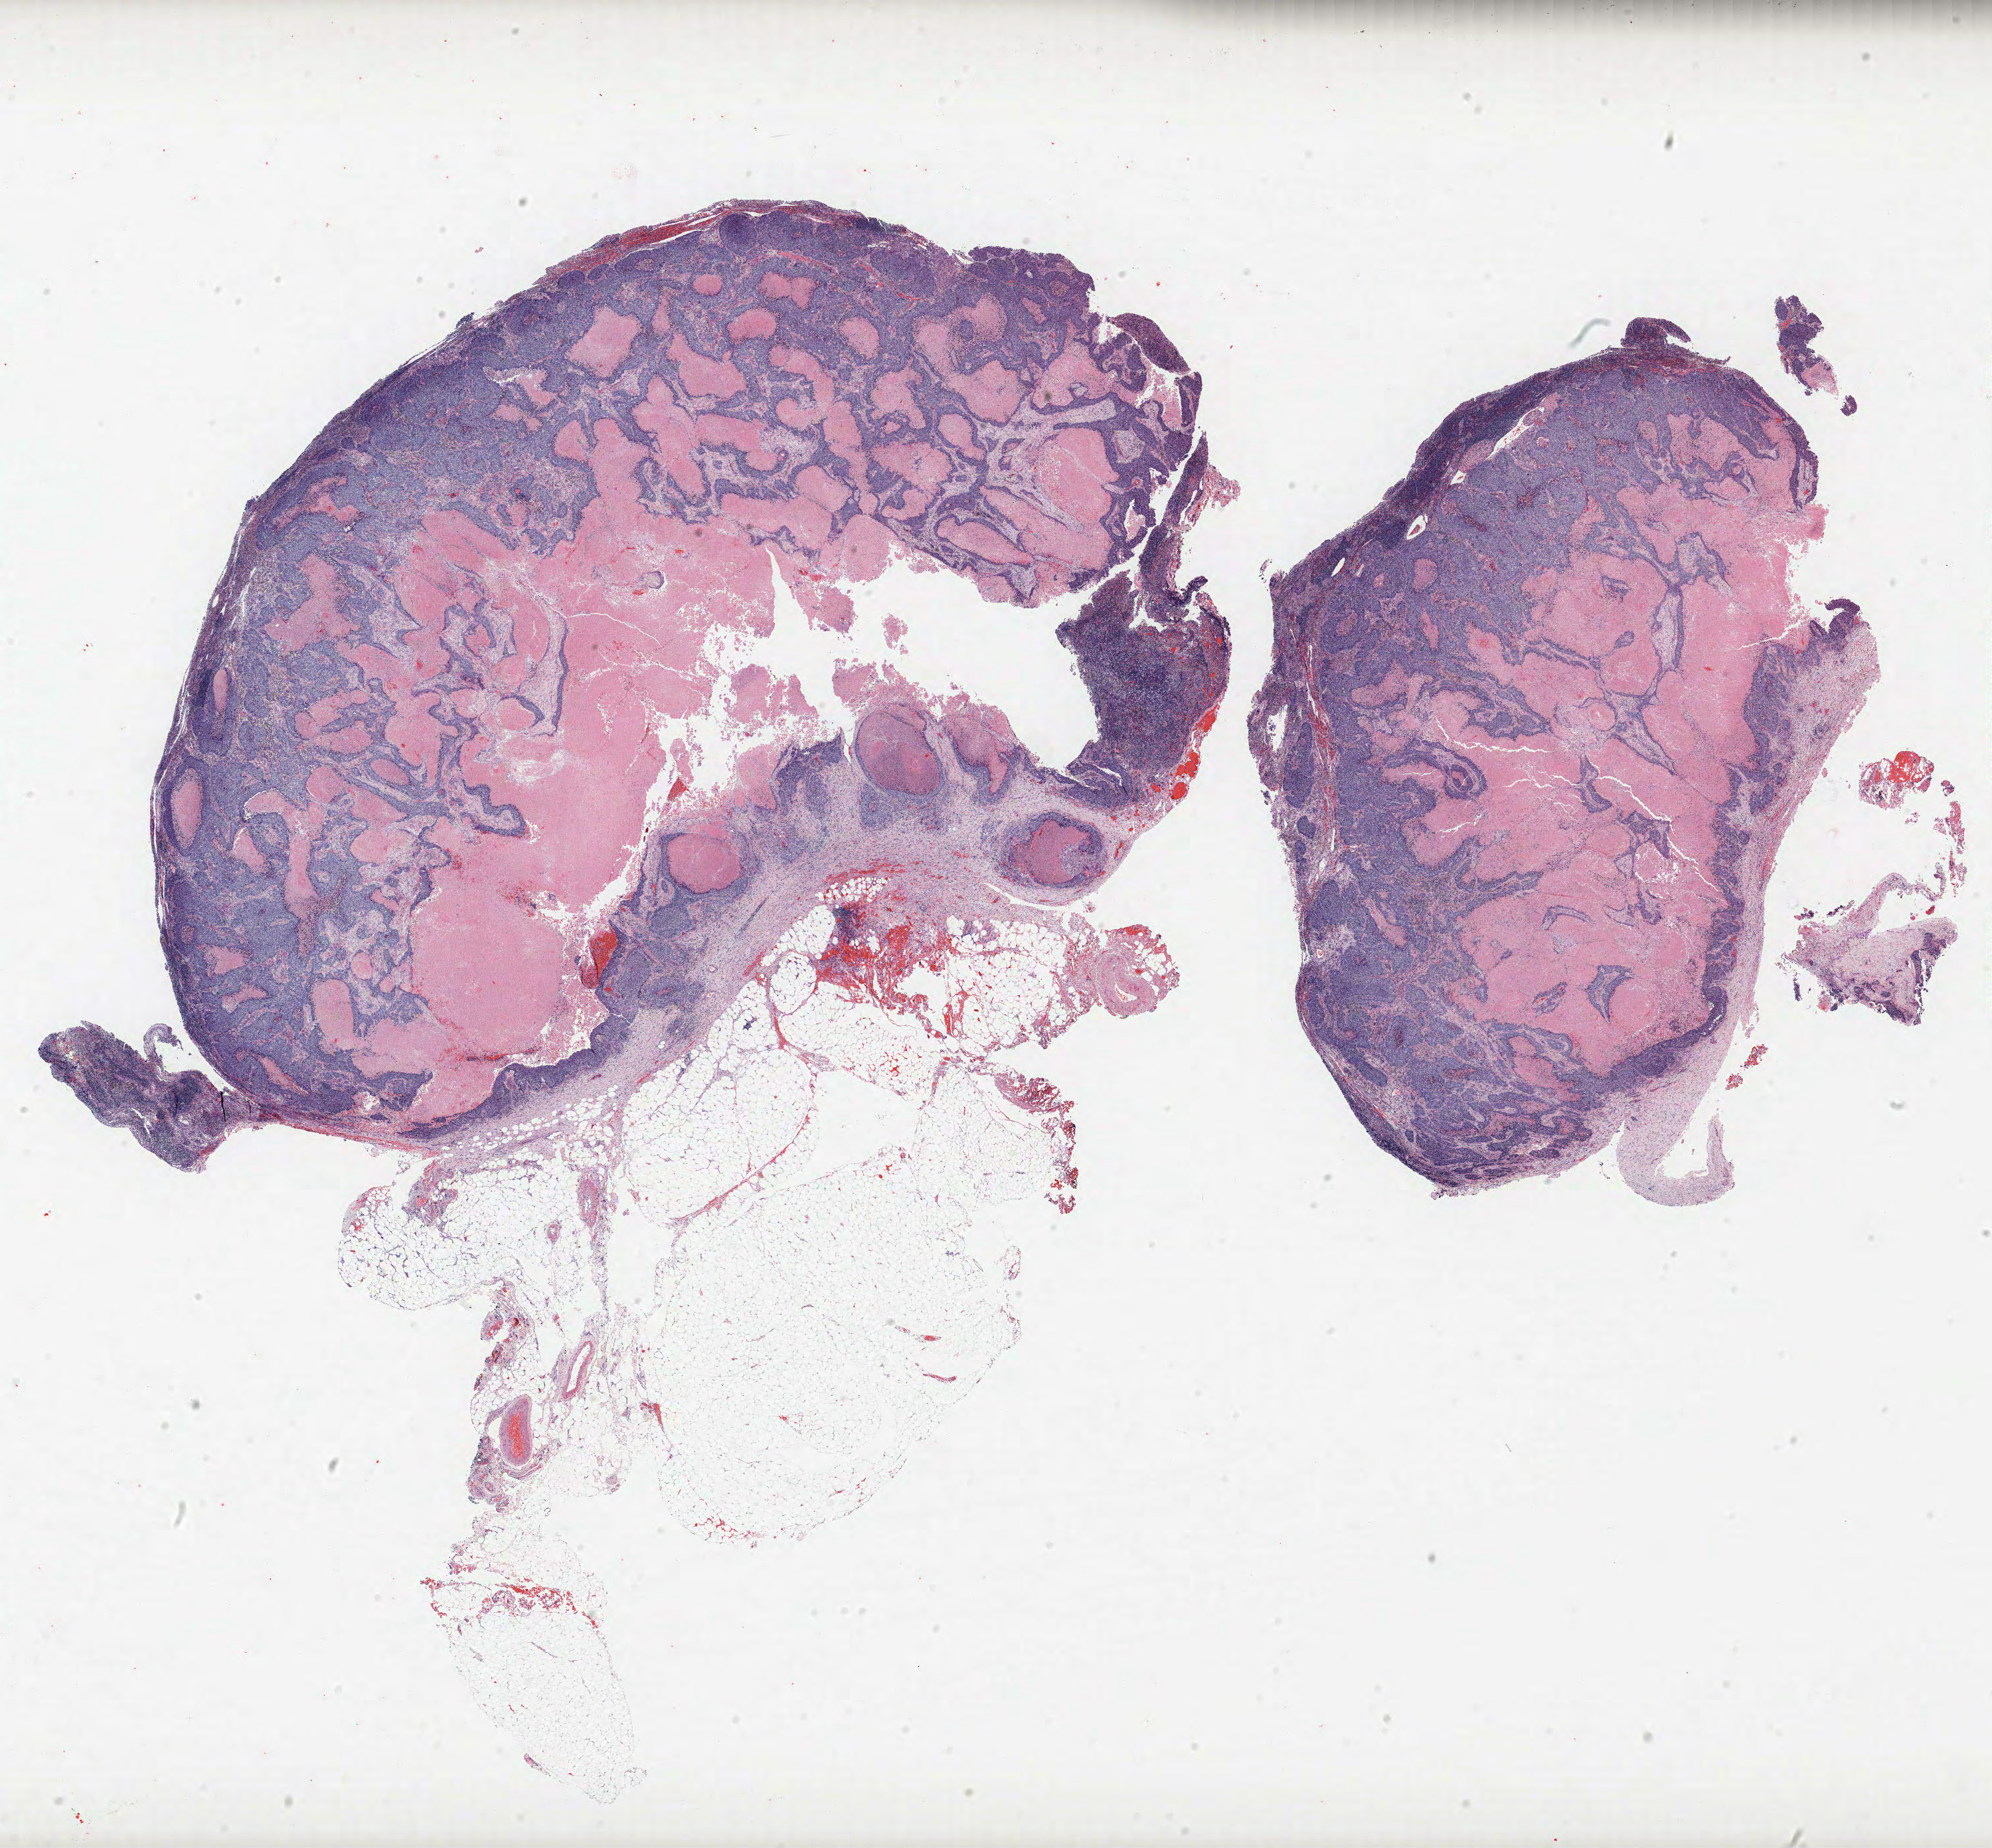
Whole-slide histology image, Hematoxylin and eosin (H&E) stained — shown as a low-resolution overview of the whole scanned area (about 24.0 x 22.3 mm, slide scanned at 40x); formalin-fixed paraffin-embedded (FFPE) section; lung tissue. Male, age 61 at enrolment. Current smoker at enrolment.
Participant's lung-cancer diagnosis: Squamous cell carcinoma, NOS (ICD-O-3 8070/3).